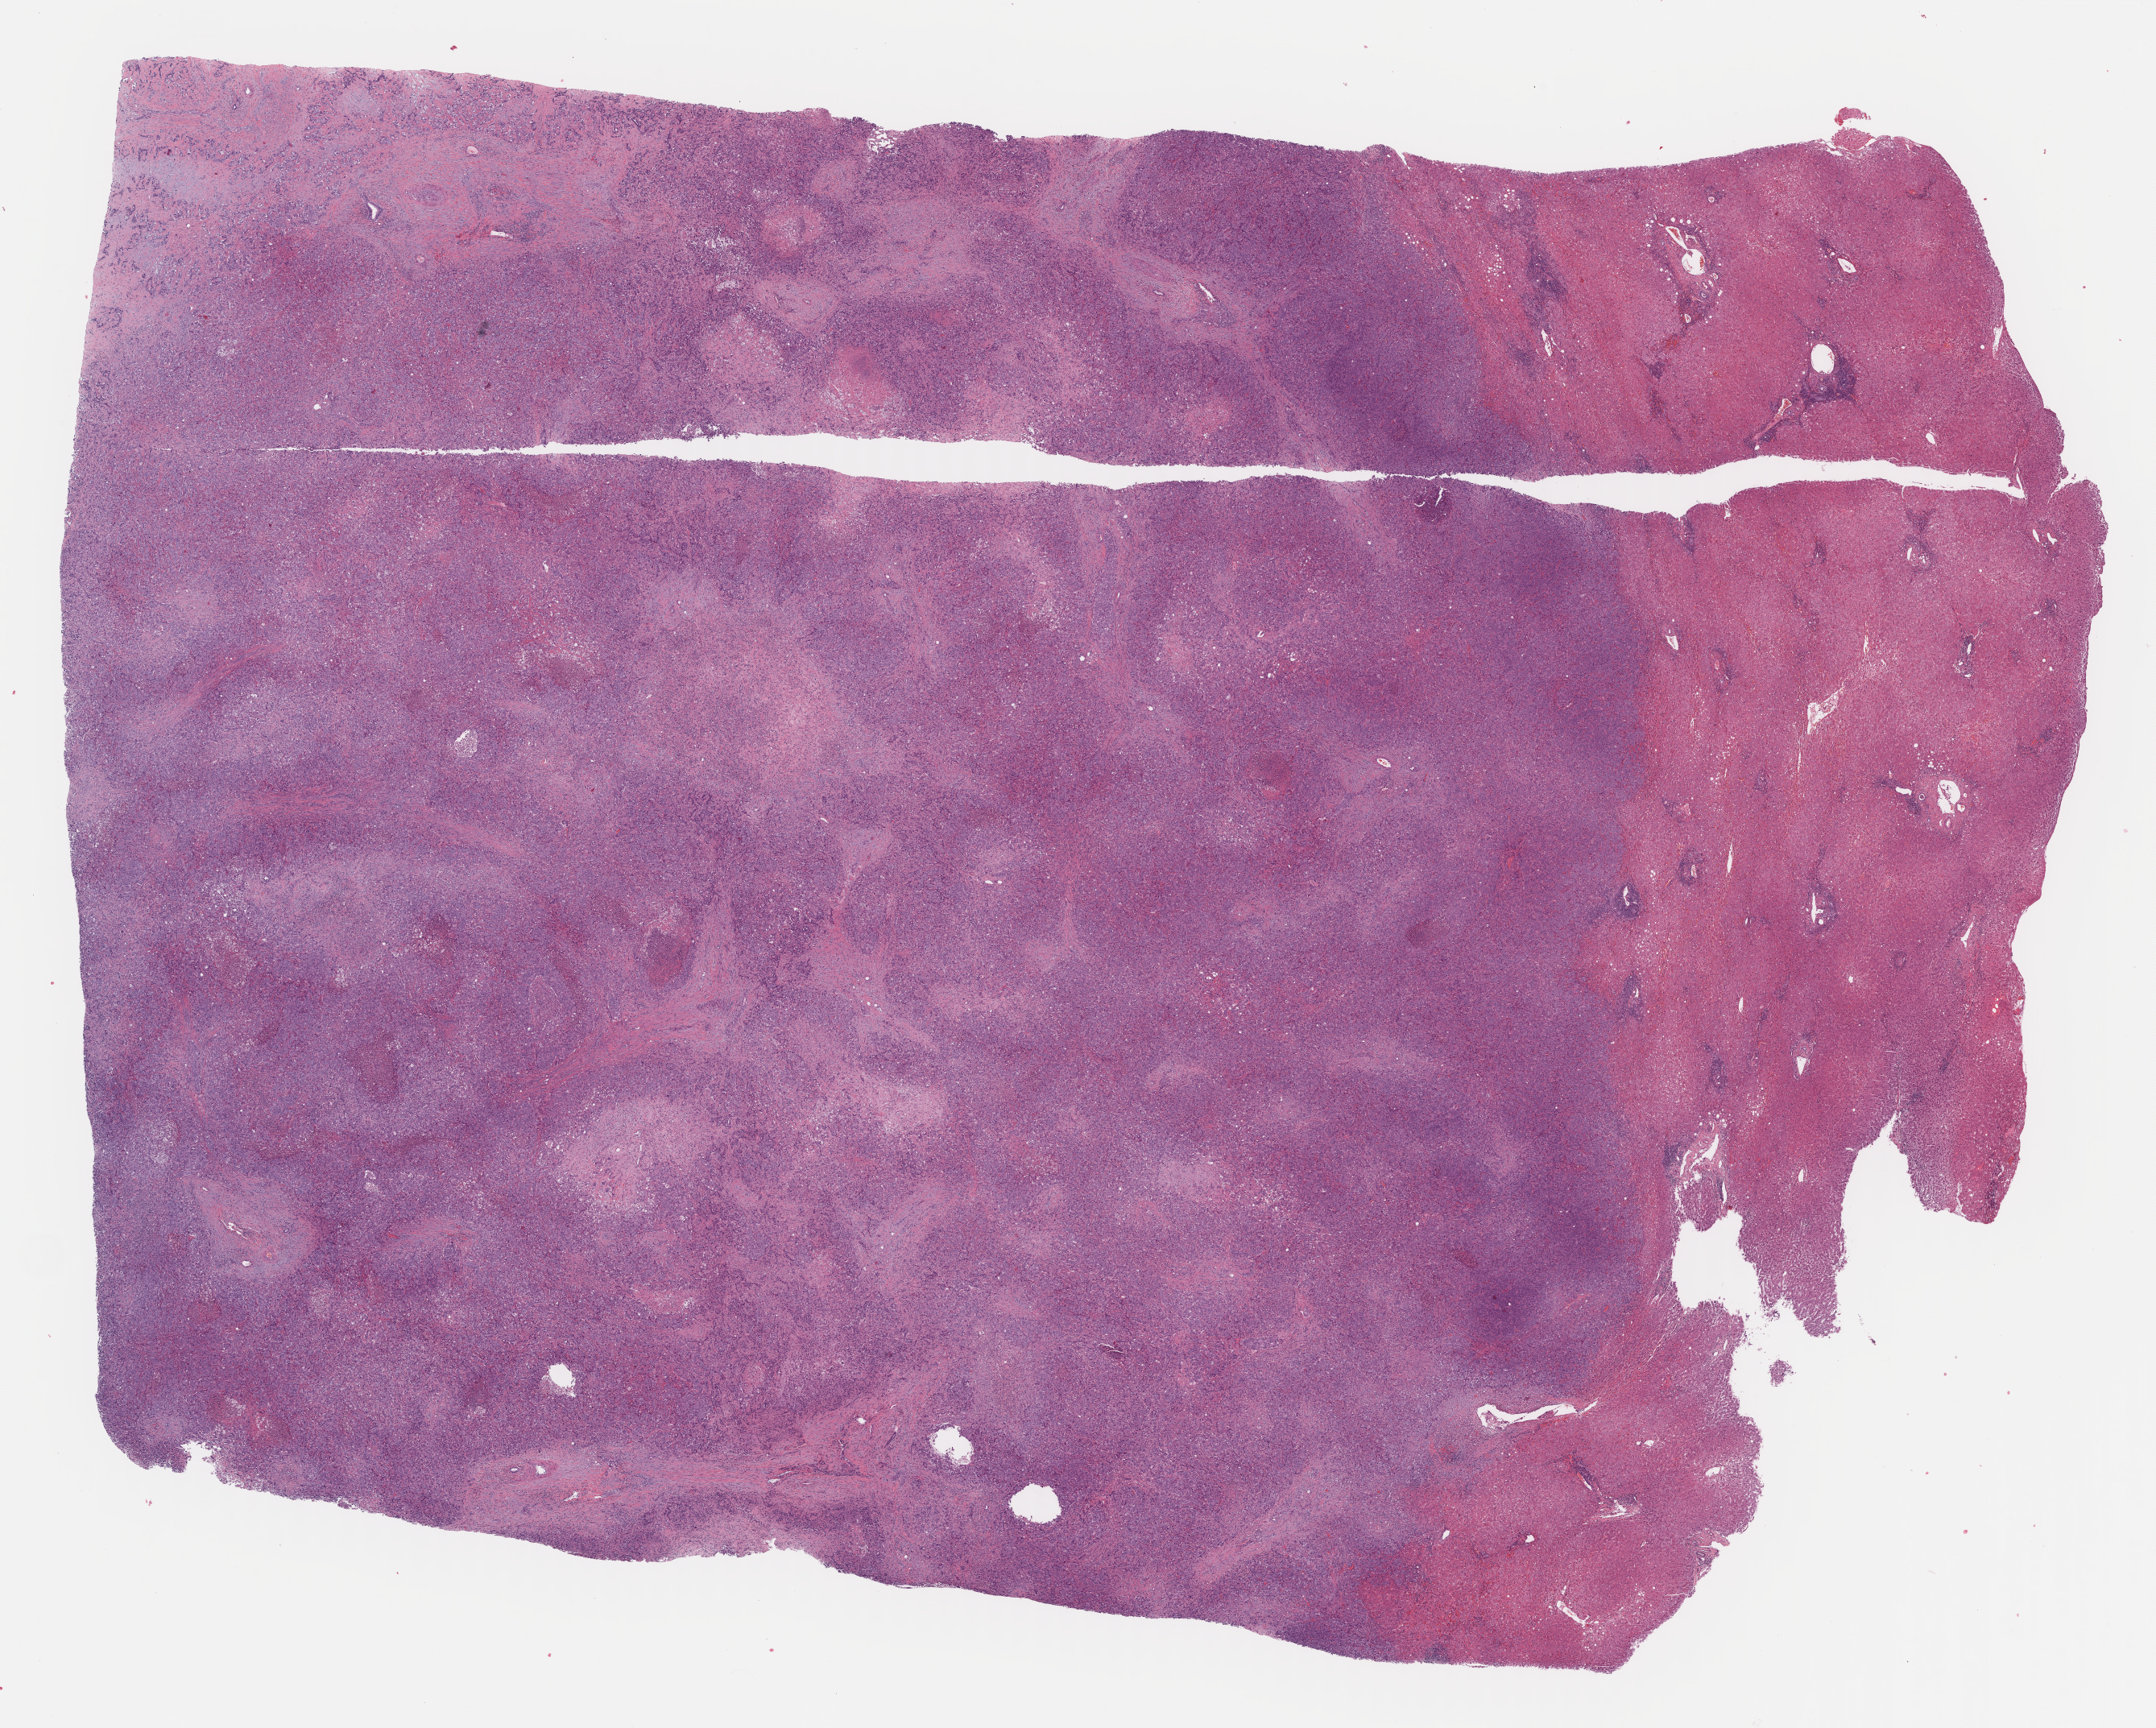
Whole-slide histology image, Hematoxylin and eosin (H&E) stained, low-resolution overview of the scanned area, about 21.7 x 17.4 mm. Formalin-fixed paraffin-embedded (FFPE) diagnostic section. Sample: primary tumour, bile duct. Male, age 71 years at initial diagnosis.
Diagnosis: Cholangiocarcinoma (intrahepatic bile duct).